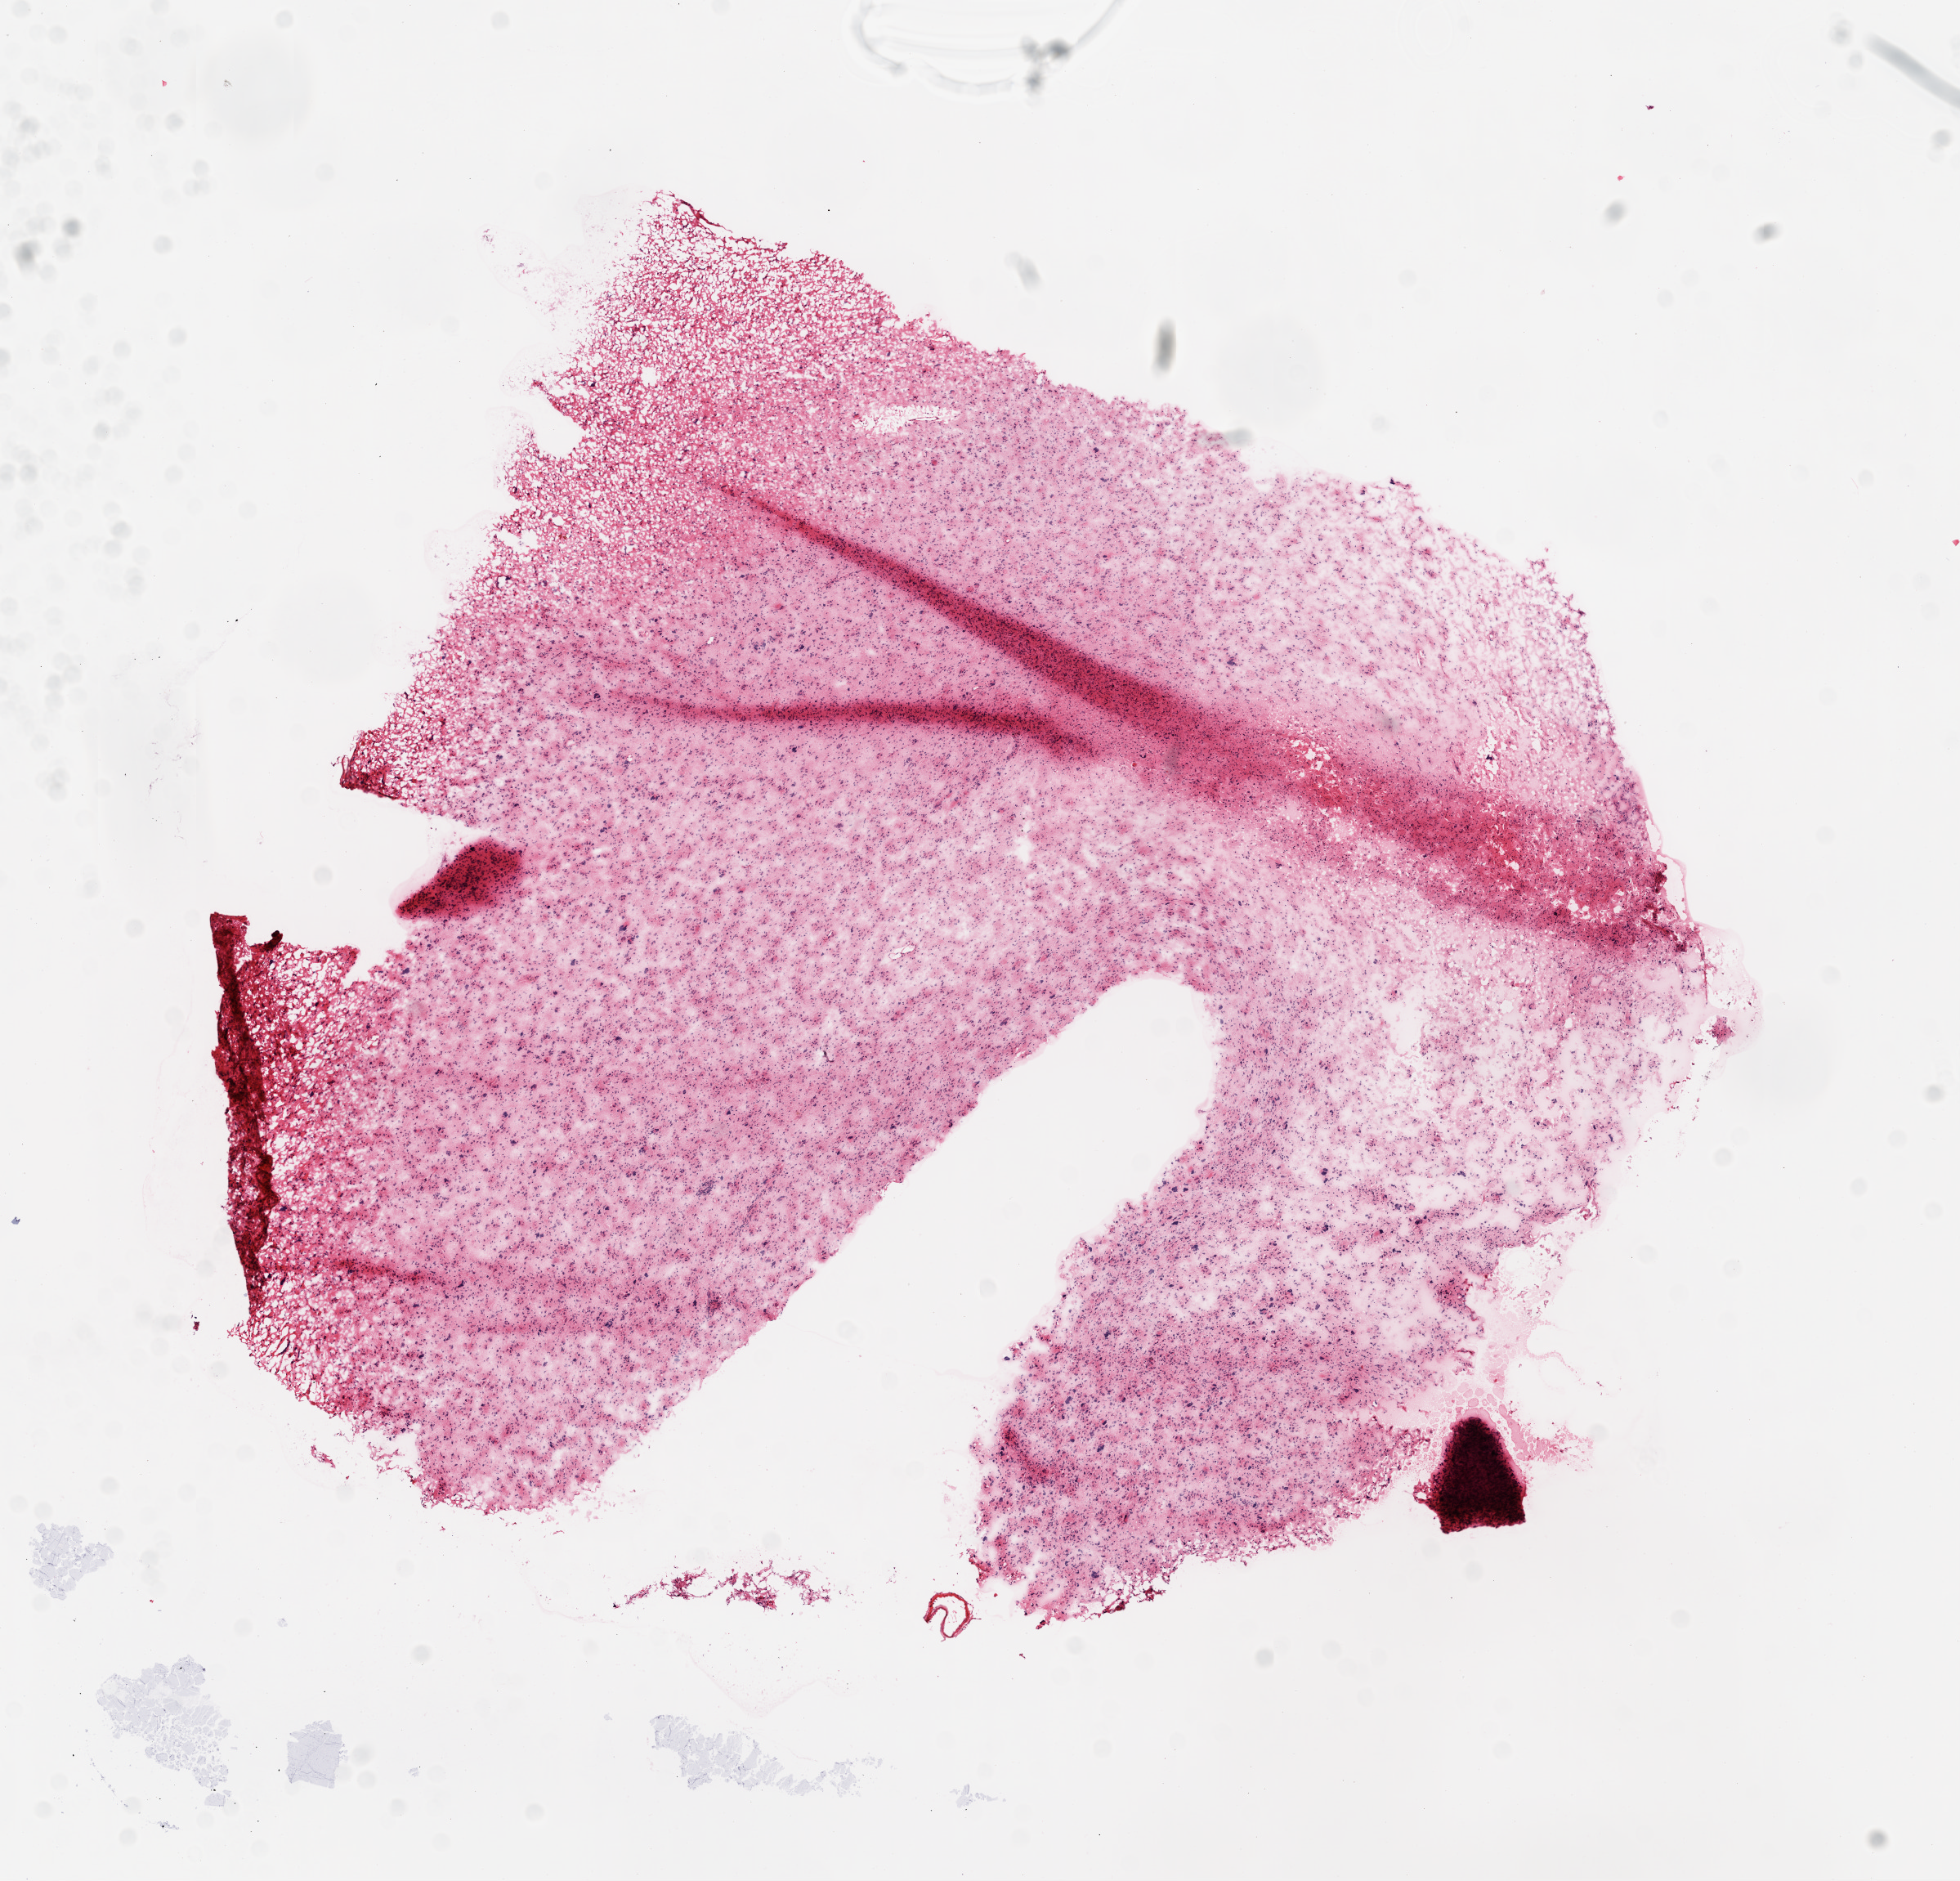
Whole-slide histology image, H&E, a low-resolution overview of the entire scanned area, about 9.7 x 9.3 mm (slide scanned at 20x). Frozen section from the bottom of the tissue portion. Brain, primary tumour sample. Male, age 46 years at initial diagnosis. Pathologist review of this section (percent, as recorded): tumour cells 80%, tumour nuclei 85%, normal cells 0%, stromal cells 10%, necrosis 10%.
Histologic diagnosis: Glioblastoma.